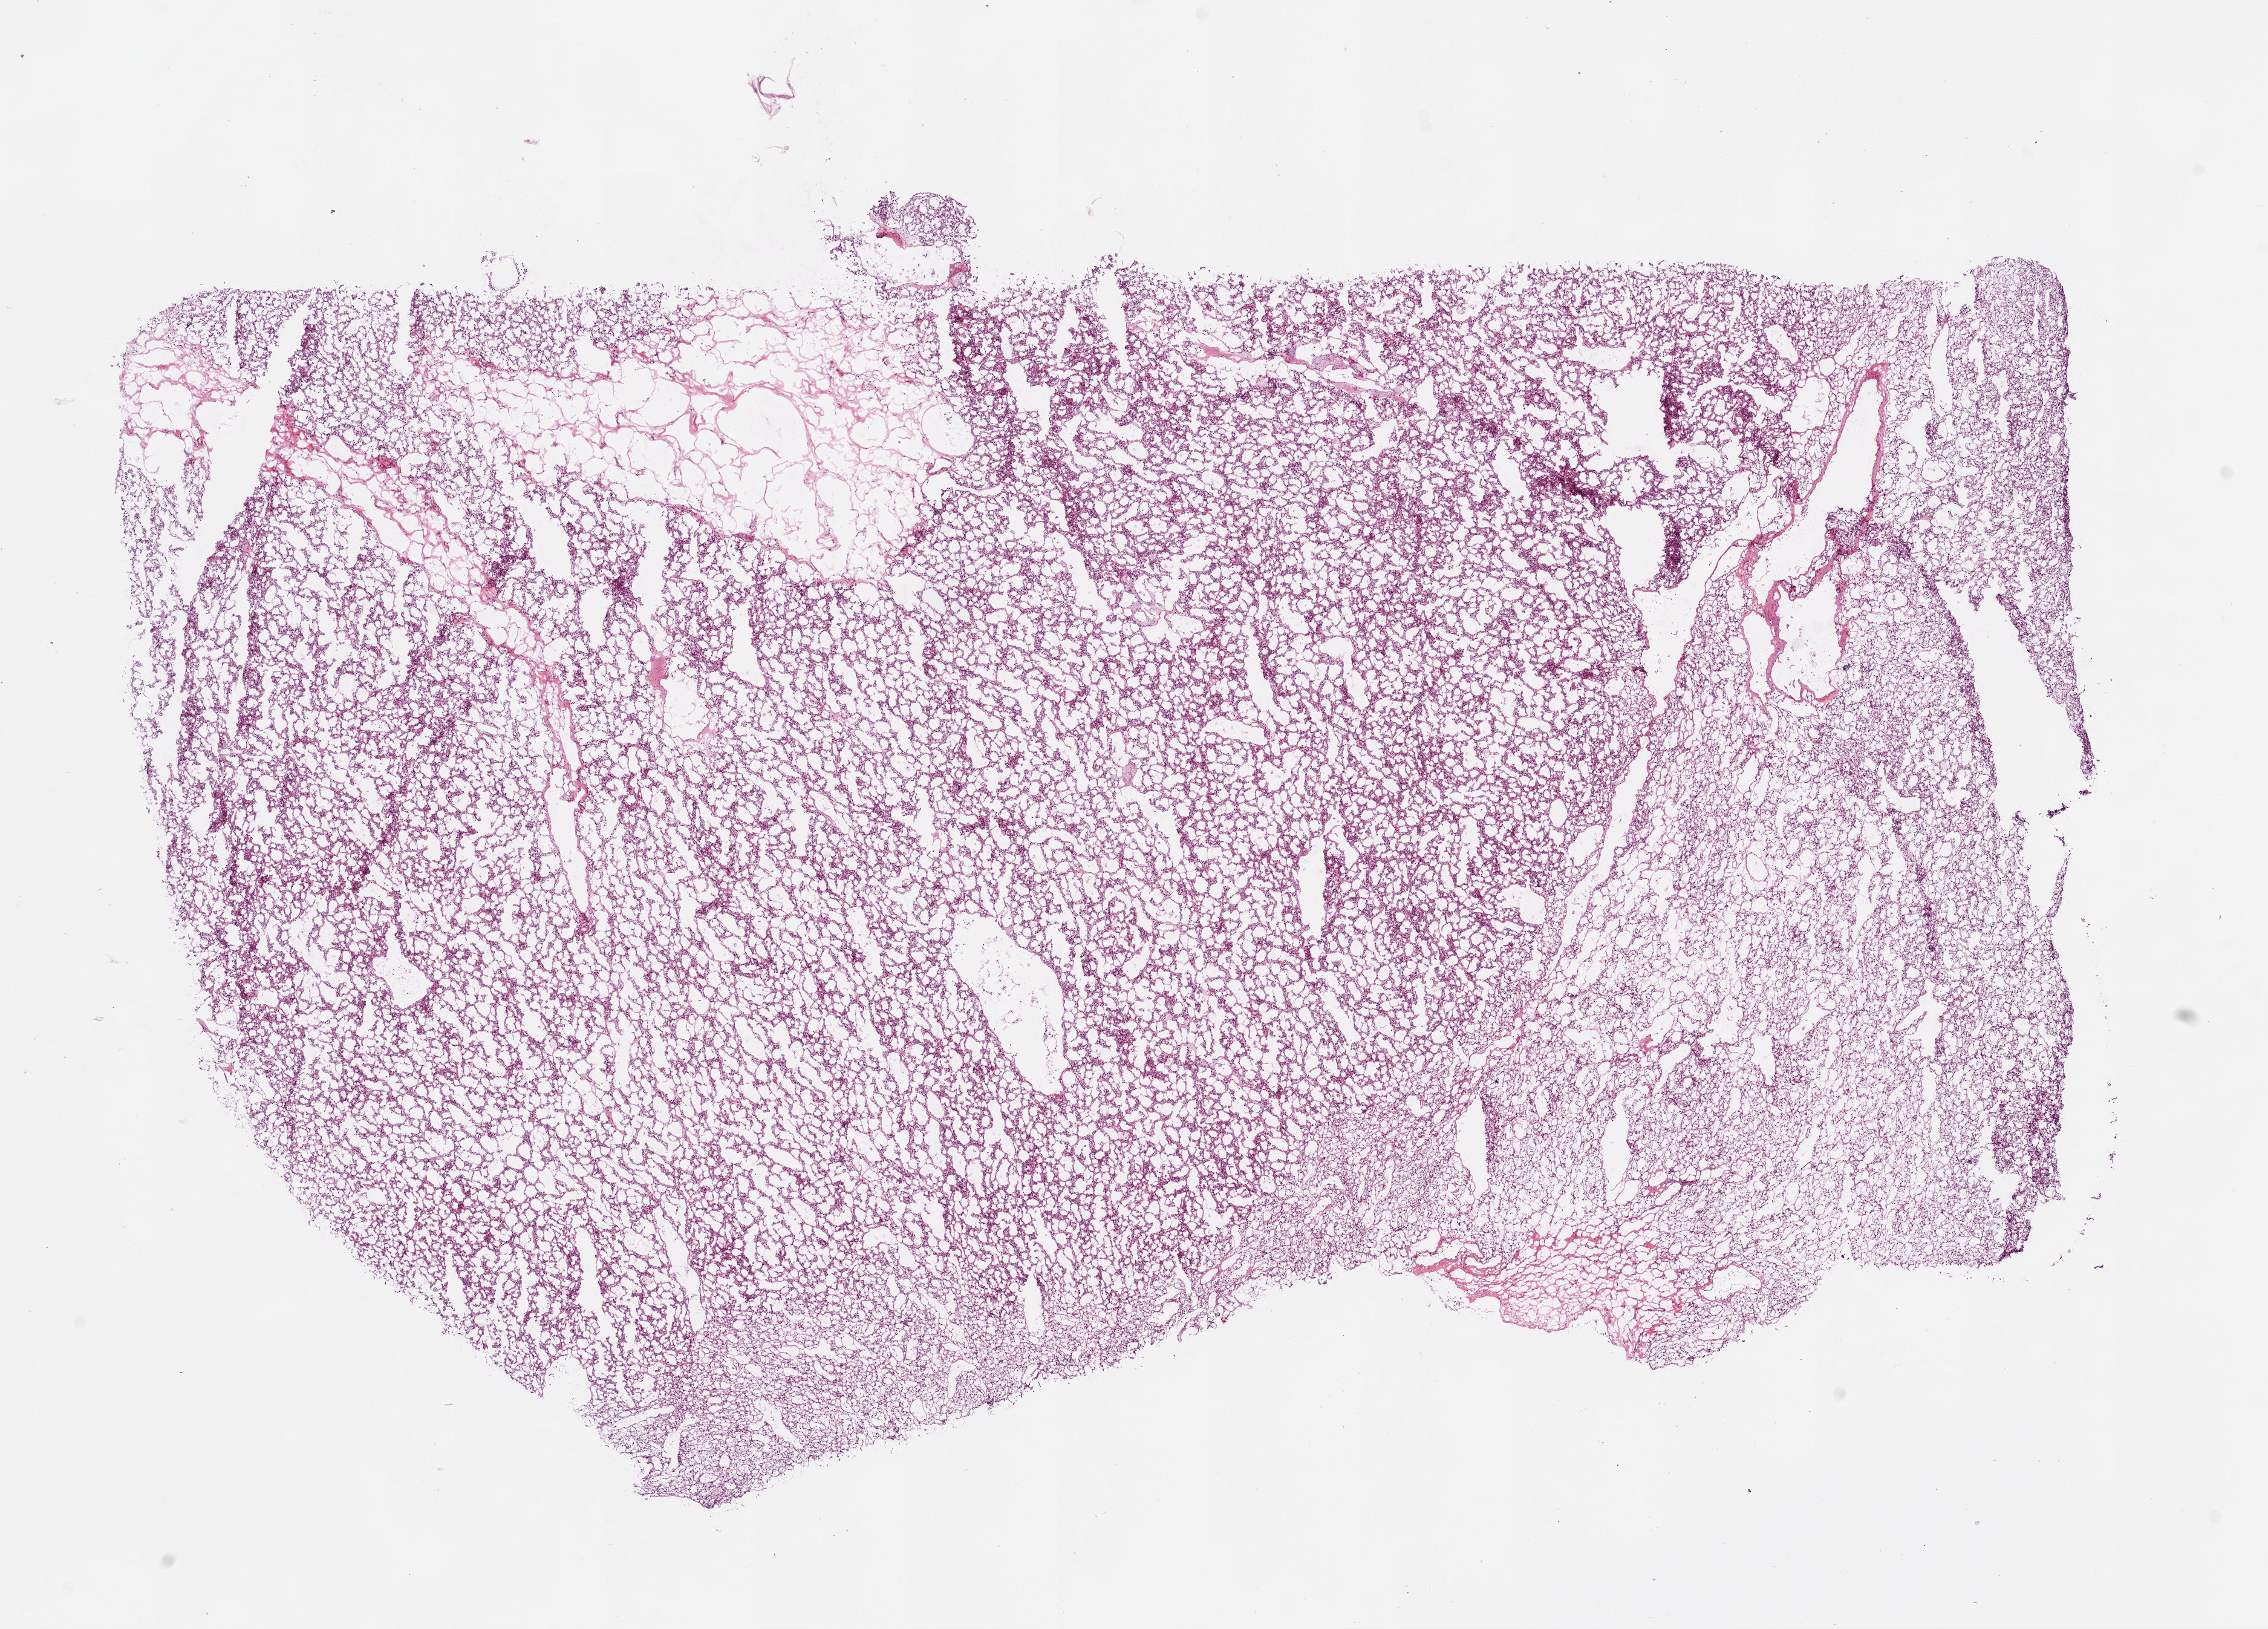
Digitized H&E tissue section (whole slide) — a low-resolution overview of the entire scanned area, about 15.0 x 10.8 mm (acquisition: 20x scan); frozen section from the bottom of the tissue portion; kidney, primary tumour sample. Female, age 43 years at initial diagnosis. Histologic grade: G2 (moderately differentiated). Composition of this section per pathologist review: tumour cells 90%, tumour nuclei 85%, normal cells 0%, stromal cells 10%, necrosis 0%.
• AJCC pathologic stage: I
• laterality: right
• TNM: T1b NX M0
• pathologic diagnosis: Clear cell adenocarcinoma, NOS